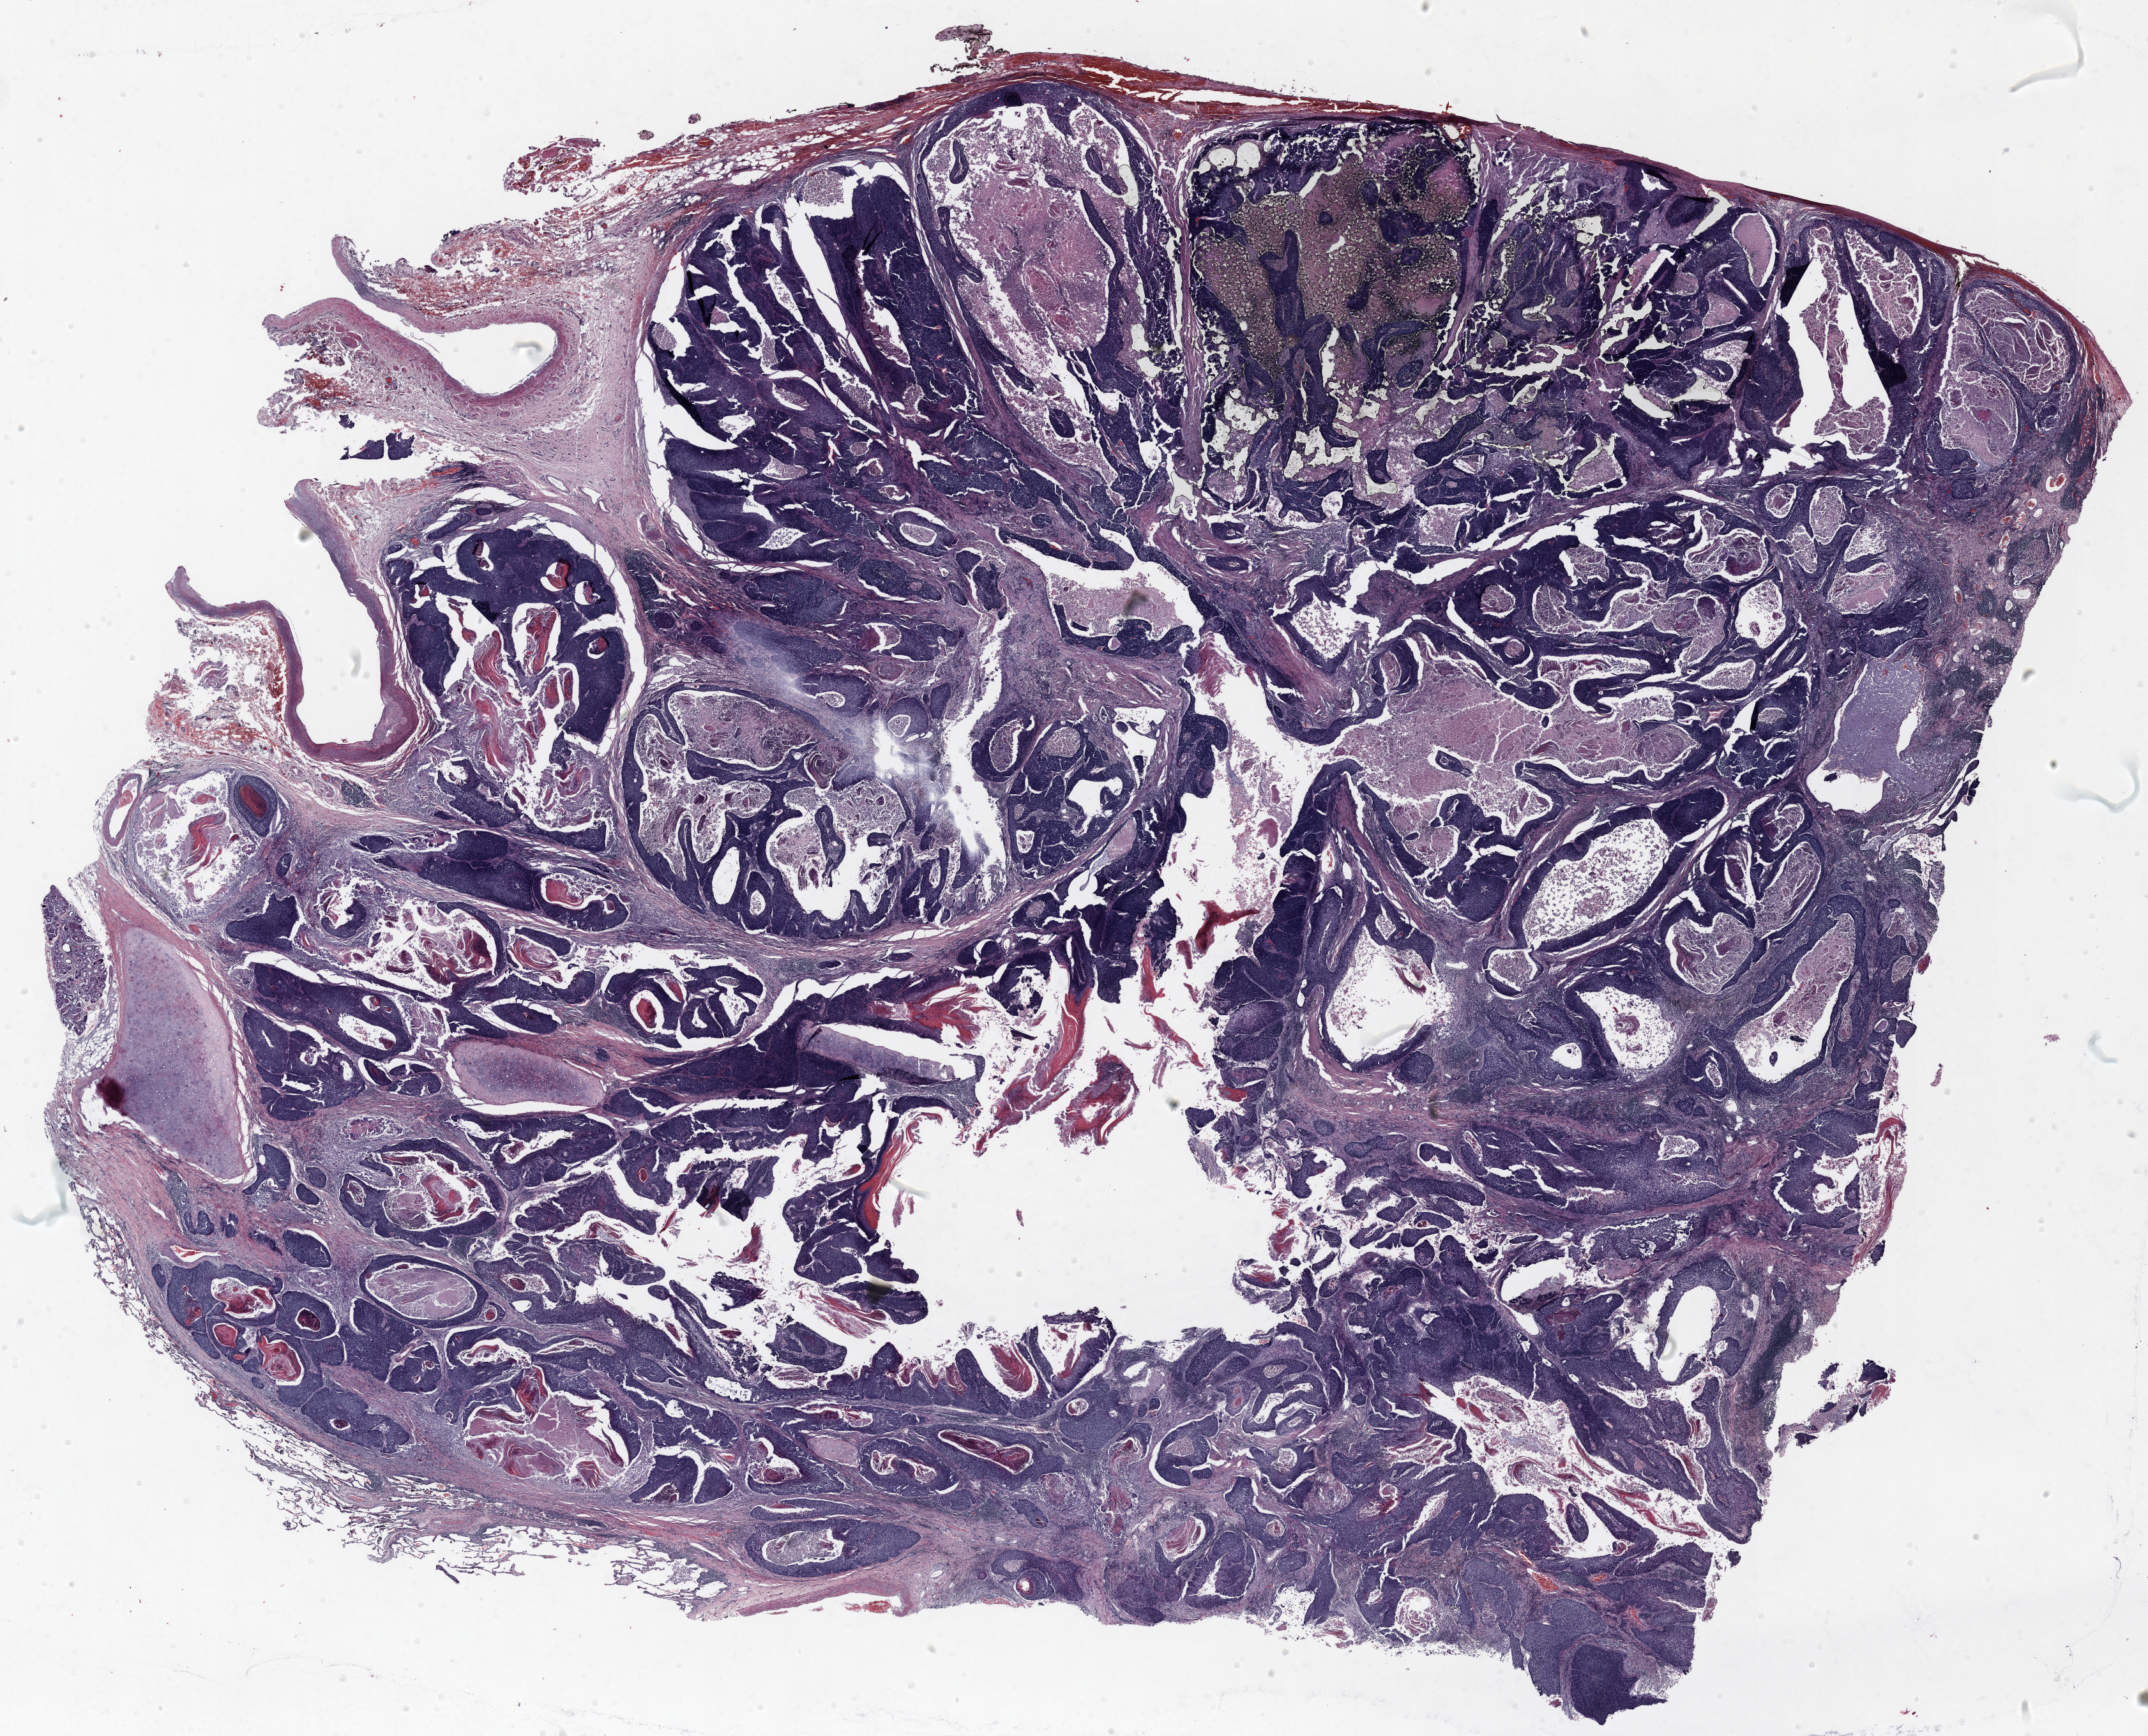
Hematoxylin and eosin (H&E) stained whole-slide image — shown as a low-resolution overview of the whole scanned area (about 27.0 x 21.8 mm, slide scanned at 20x); formalin-fixed paraffin-embedded (FFPE) section; lung. Male, age 70 at enrolment. Grade: poorly differentiated (G3).
Stage (AJCC 6th edition): IB. Tumour size (pathology): 47 mm. Primary tumour location (clinical record): left upper lobe. Participant's lung-cancer diagnosis: Squamous cell carcinoma, NOS.